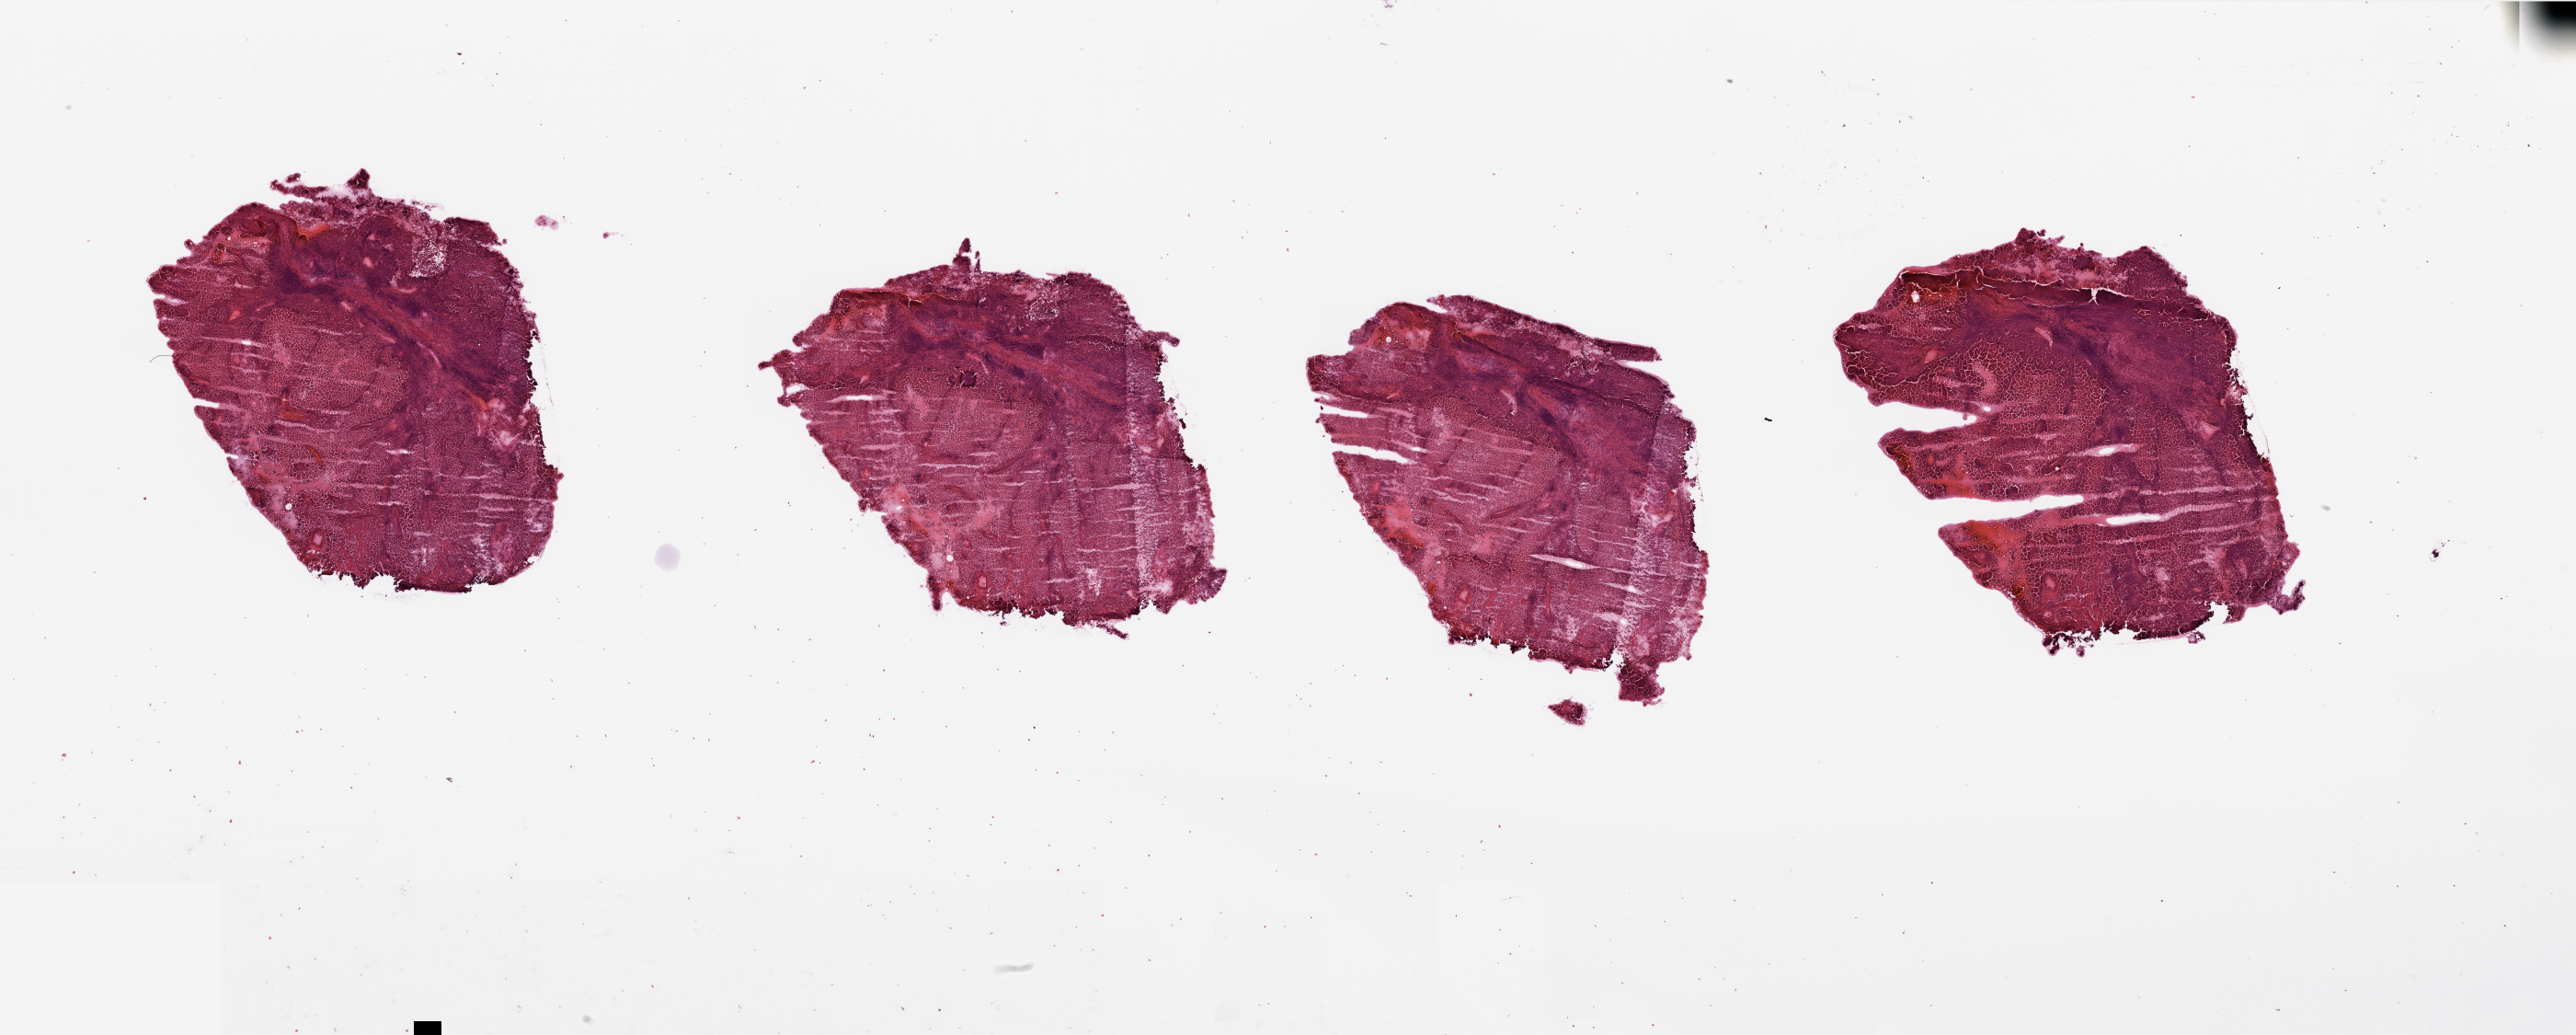
Digitized H&E-stained tissue section (whole slide), shown as a low-resolution overview of the whole scanned area (about 44.3 x 17.8 mm, acquisition: 20x scan), tumour tissue sample, sampled site: kidney. Female, 74 y/o. Histologic grade: G2 (moderately differentiated). Slide review estimates, as recorded: tumour nuclei 80%, necrosis 10%.
Diagnosis: Renal cell carcinoma, NOS. Primary tumour site (as recorded): lower pole. AJCC pathologic stage: I.